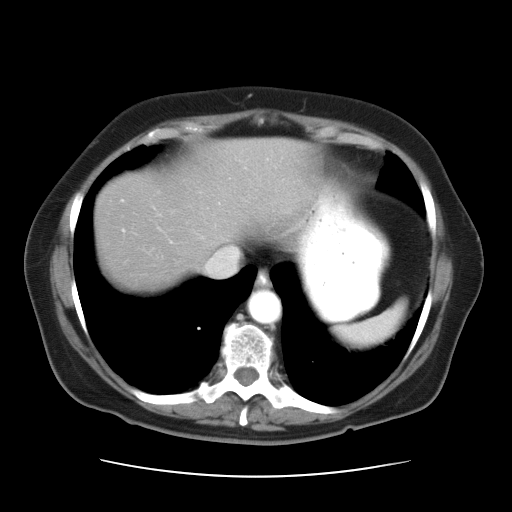
Contrast-enhanced abdominal CT, one axial slice. Position 29 of 34 along the scan axis. Reconstruction kernel STANDARD. 120 kVp. Intravenous contrast given. Soft-tissue window (W 400 / L 40 HU). 7.5 mm slice thickness. 512 × 512 image matrix, field of view 360 × 360 mm. Female patient, age 65 years. Case-level facts recorded for this patient, not image findings: diagnosis: colorectal cancer liver metastases, imaged before liver resection; multiple liver metastases: yes; largest metastasis: 2.2 cm; disease in both lobes: no.
Annotated regions visible in this slice (expert manual segmentation):
- hepatic veins: bounding box (x1, y1, x2, y2) in pixels: (206, 247, 239, 277)
- liver: (98, 143, 301, 287)
- planned liver remnant (the part of the liver to remain after resection): (98, 144, 302, 287)